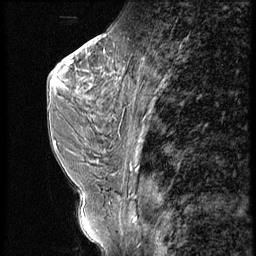
Breast MRI (dynamic contrast-enhanced), one sagittal slice. Slice 27 of 56 in the series (ordered by position). 4 images stored at this slice position (order not interpretable as contrast timing). 1.5 T. TE 4.2 ms, TR 9 ms. 2.5 mm slice thickness. 256 × 256 image matrix. Patient: female, 44 years. Case-level facts recorded for this patient, not image findings: setting: breast cancer imaged before/during neoadjuvant chemotherapy; receptor status: triple-negative.
Annotated regions visible in this slice (semi-automatically segmented with operator editing):
- analysis volume of interest (the breast-tissue region the enhancement analysis was run in; not a lesion): bounding box (x1, y1, x2, y2) in pixels: (87, 28, 132, 99)
- tumour enhancement mask (voxels above the 140 % enhancement threshold inside the analysis volume of interest): (87, 72, 110, 84)